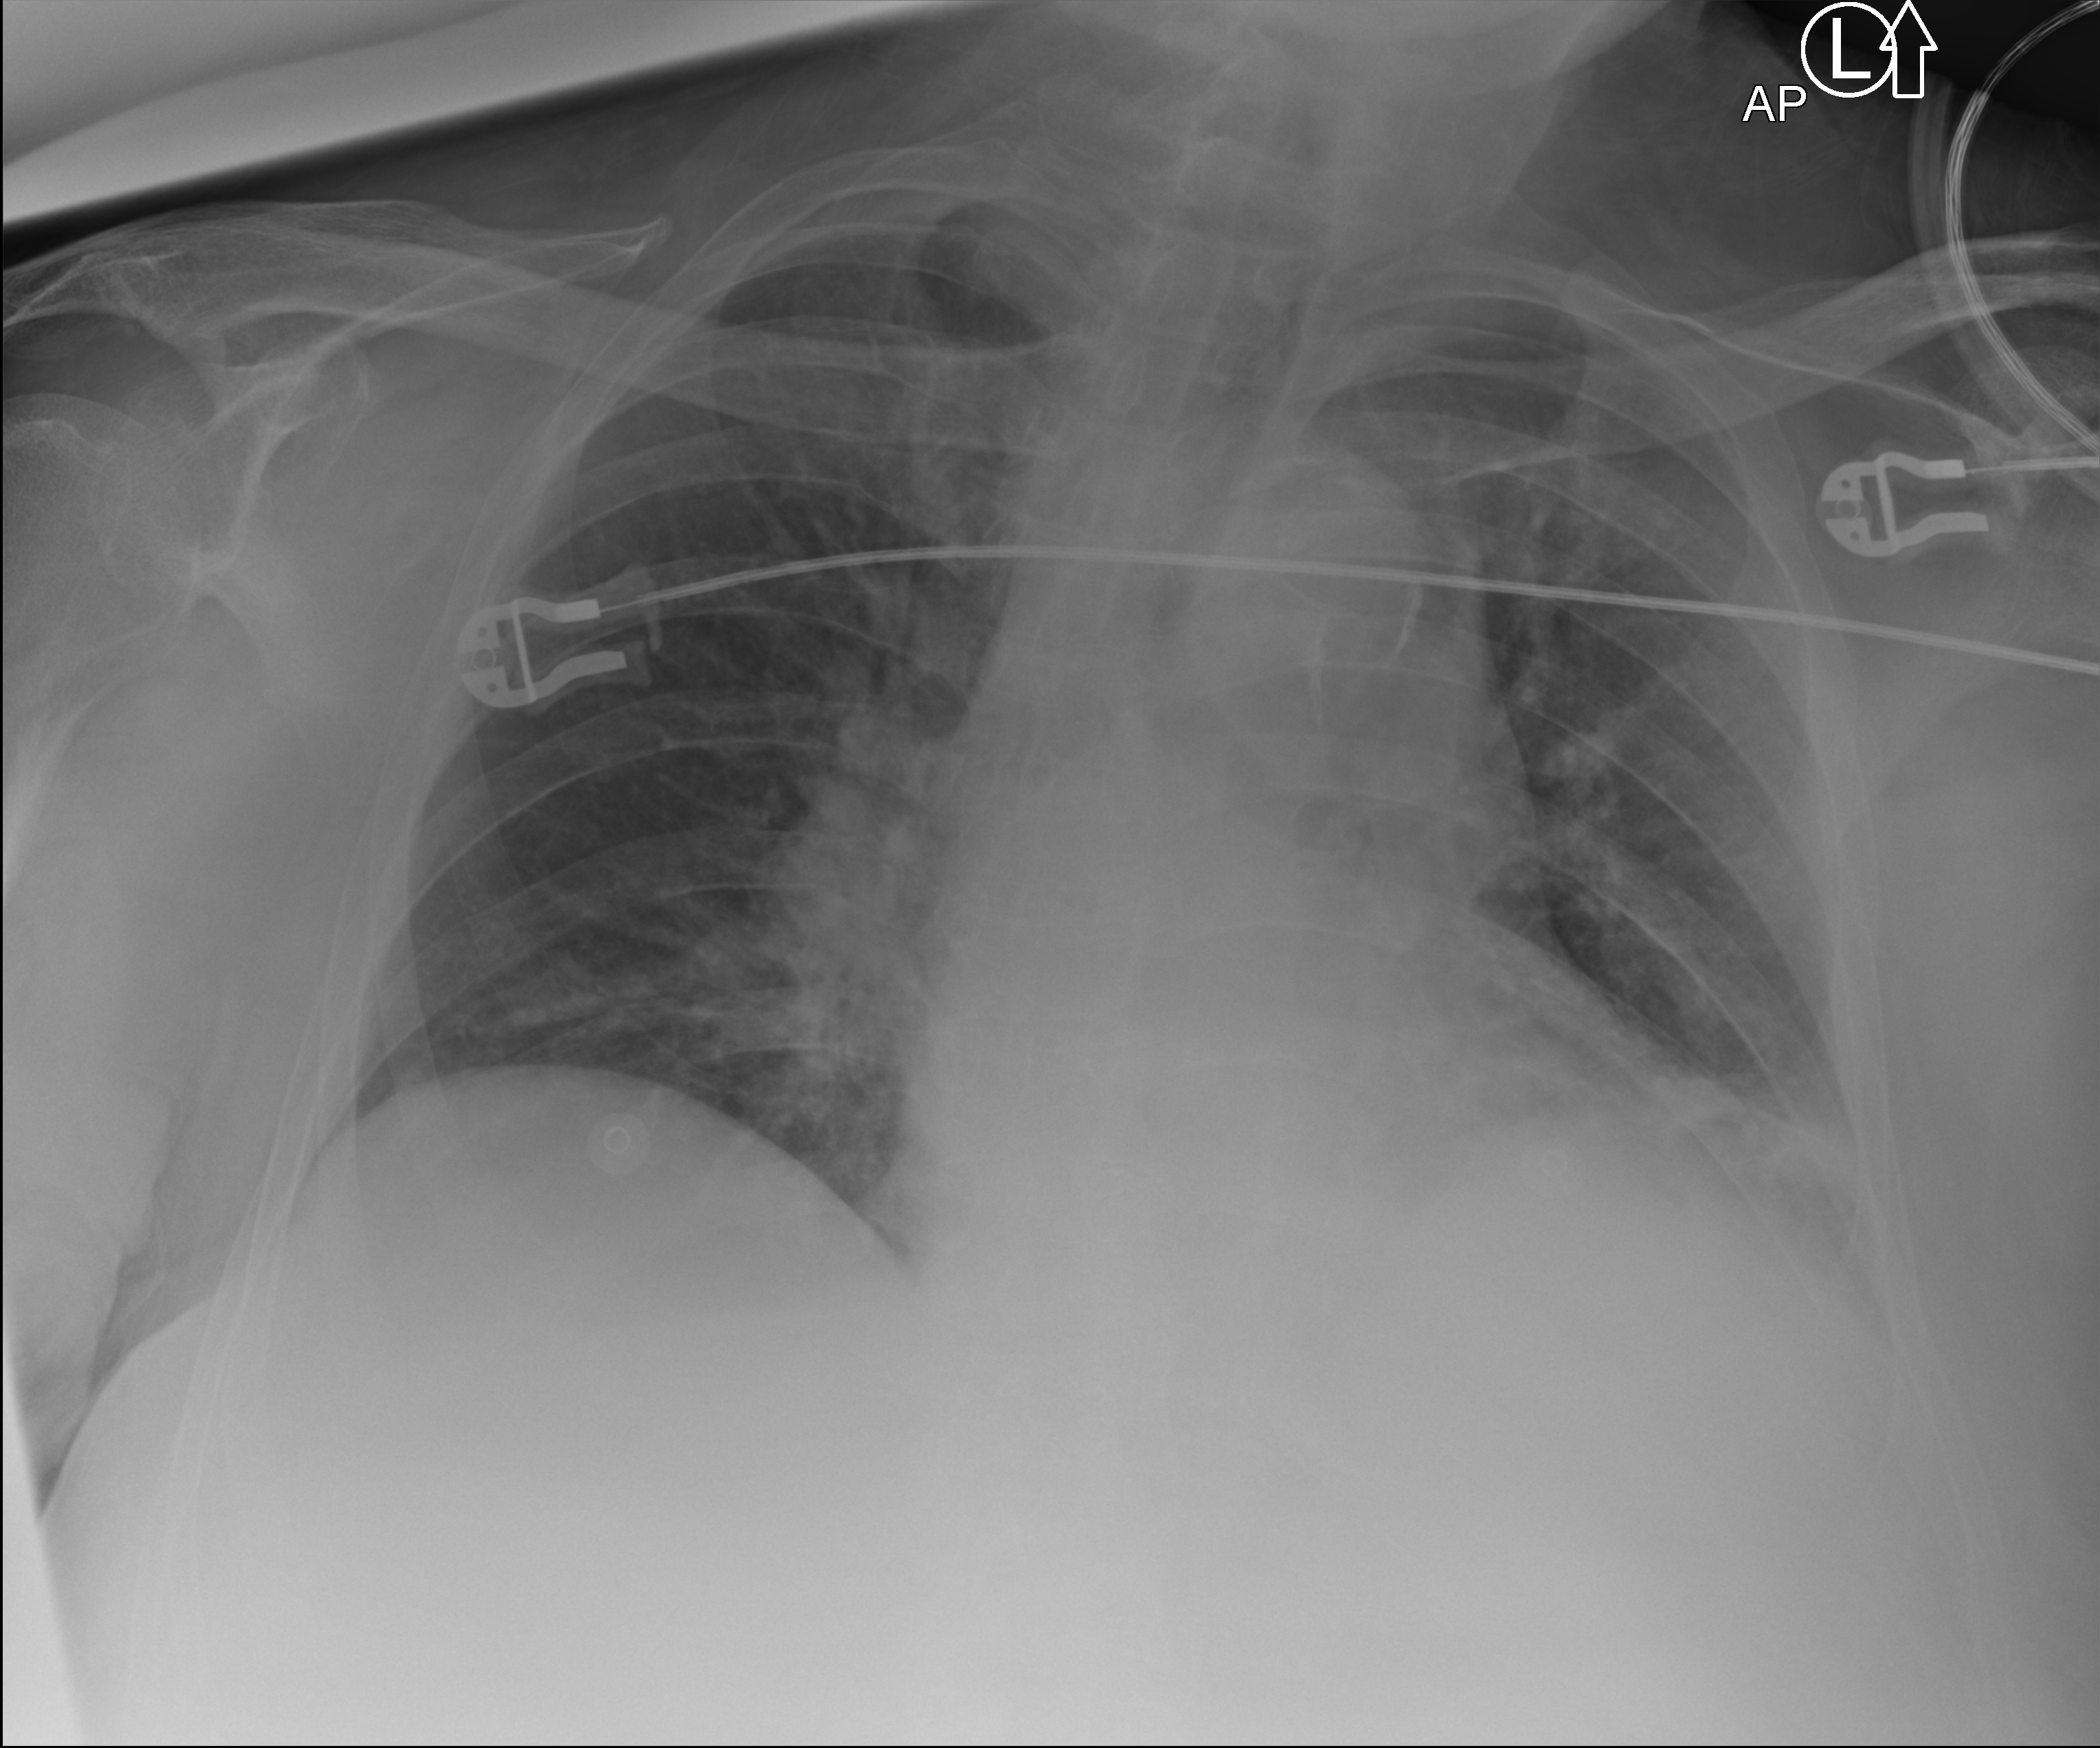
Bedside chest radiograph (computed radiography), anteroposterior (AP) projection. Male patient hospitalised with COVID-19, age 75–90 years.
Admission-level facts for this patient (not findings on this image; timing relative to this image not recorded): hypertension (admission record): no; mechanically ventilated during this hospital stay: no.